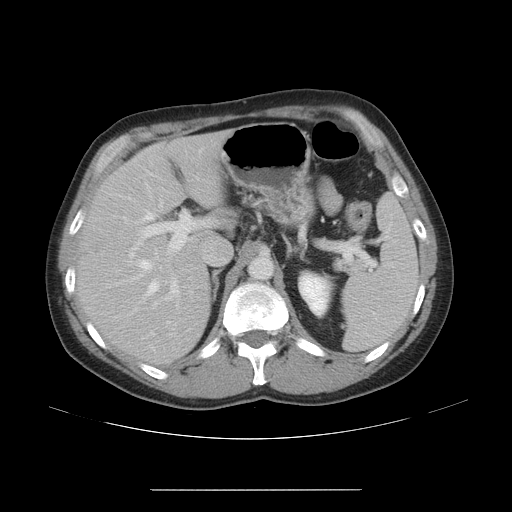
Contrast-enhanced abdominal CT, one axial slice; slice 30 of 48 in the series (ordered by position); reconstruction kernel STANDARD; 120 kVp; intravenous contrast given; soft-tissue window (W 400 / L 40 HU); 5 mm slice thickness; 512 × 512 image matrix. Male patient, age 56 years. Case-level facts recorded for this patient, not image findings: diagnosis: colorectal cancer liver metastases, imaged before liver resection; multiple liver metastases: yes; largest metastasis: 1.8 cm; disease in both lobes: yes.
Outlined on this slice (manually delineated by an expert):
- hepatic veins: box from (x=113, y=182) to (x=171, y=336) px
- liver: (x=78, y=134)–(x=224, y=365)
- planned liver remnant (the part of the liver to remain after resection): (x=79, y=133)–(x=225, y=365)
- portal vein (with intrahepatic branches): (x=109, y=172)–(x=217, y=306)